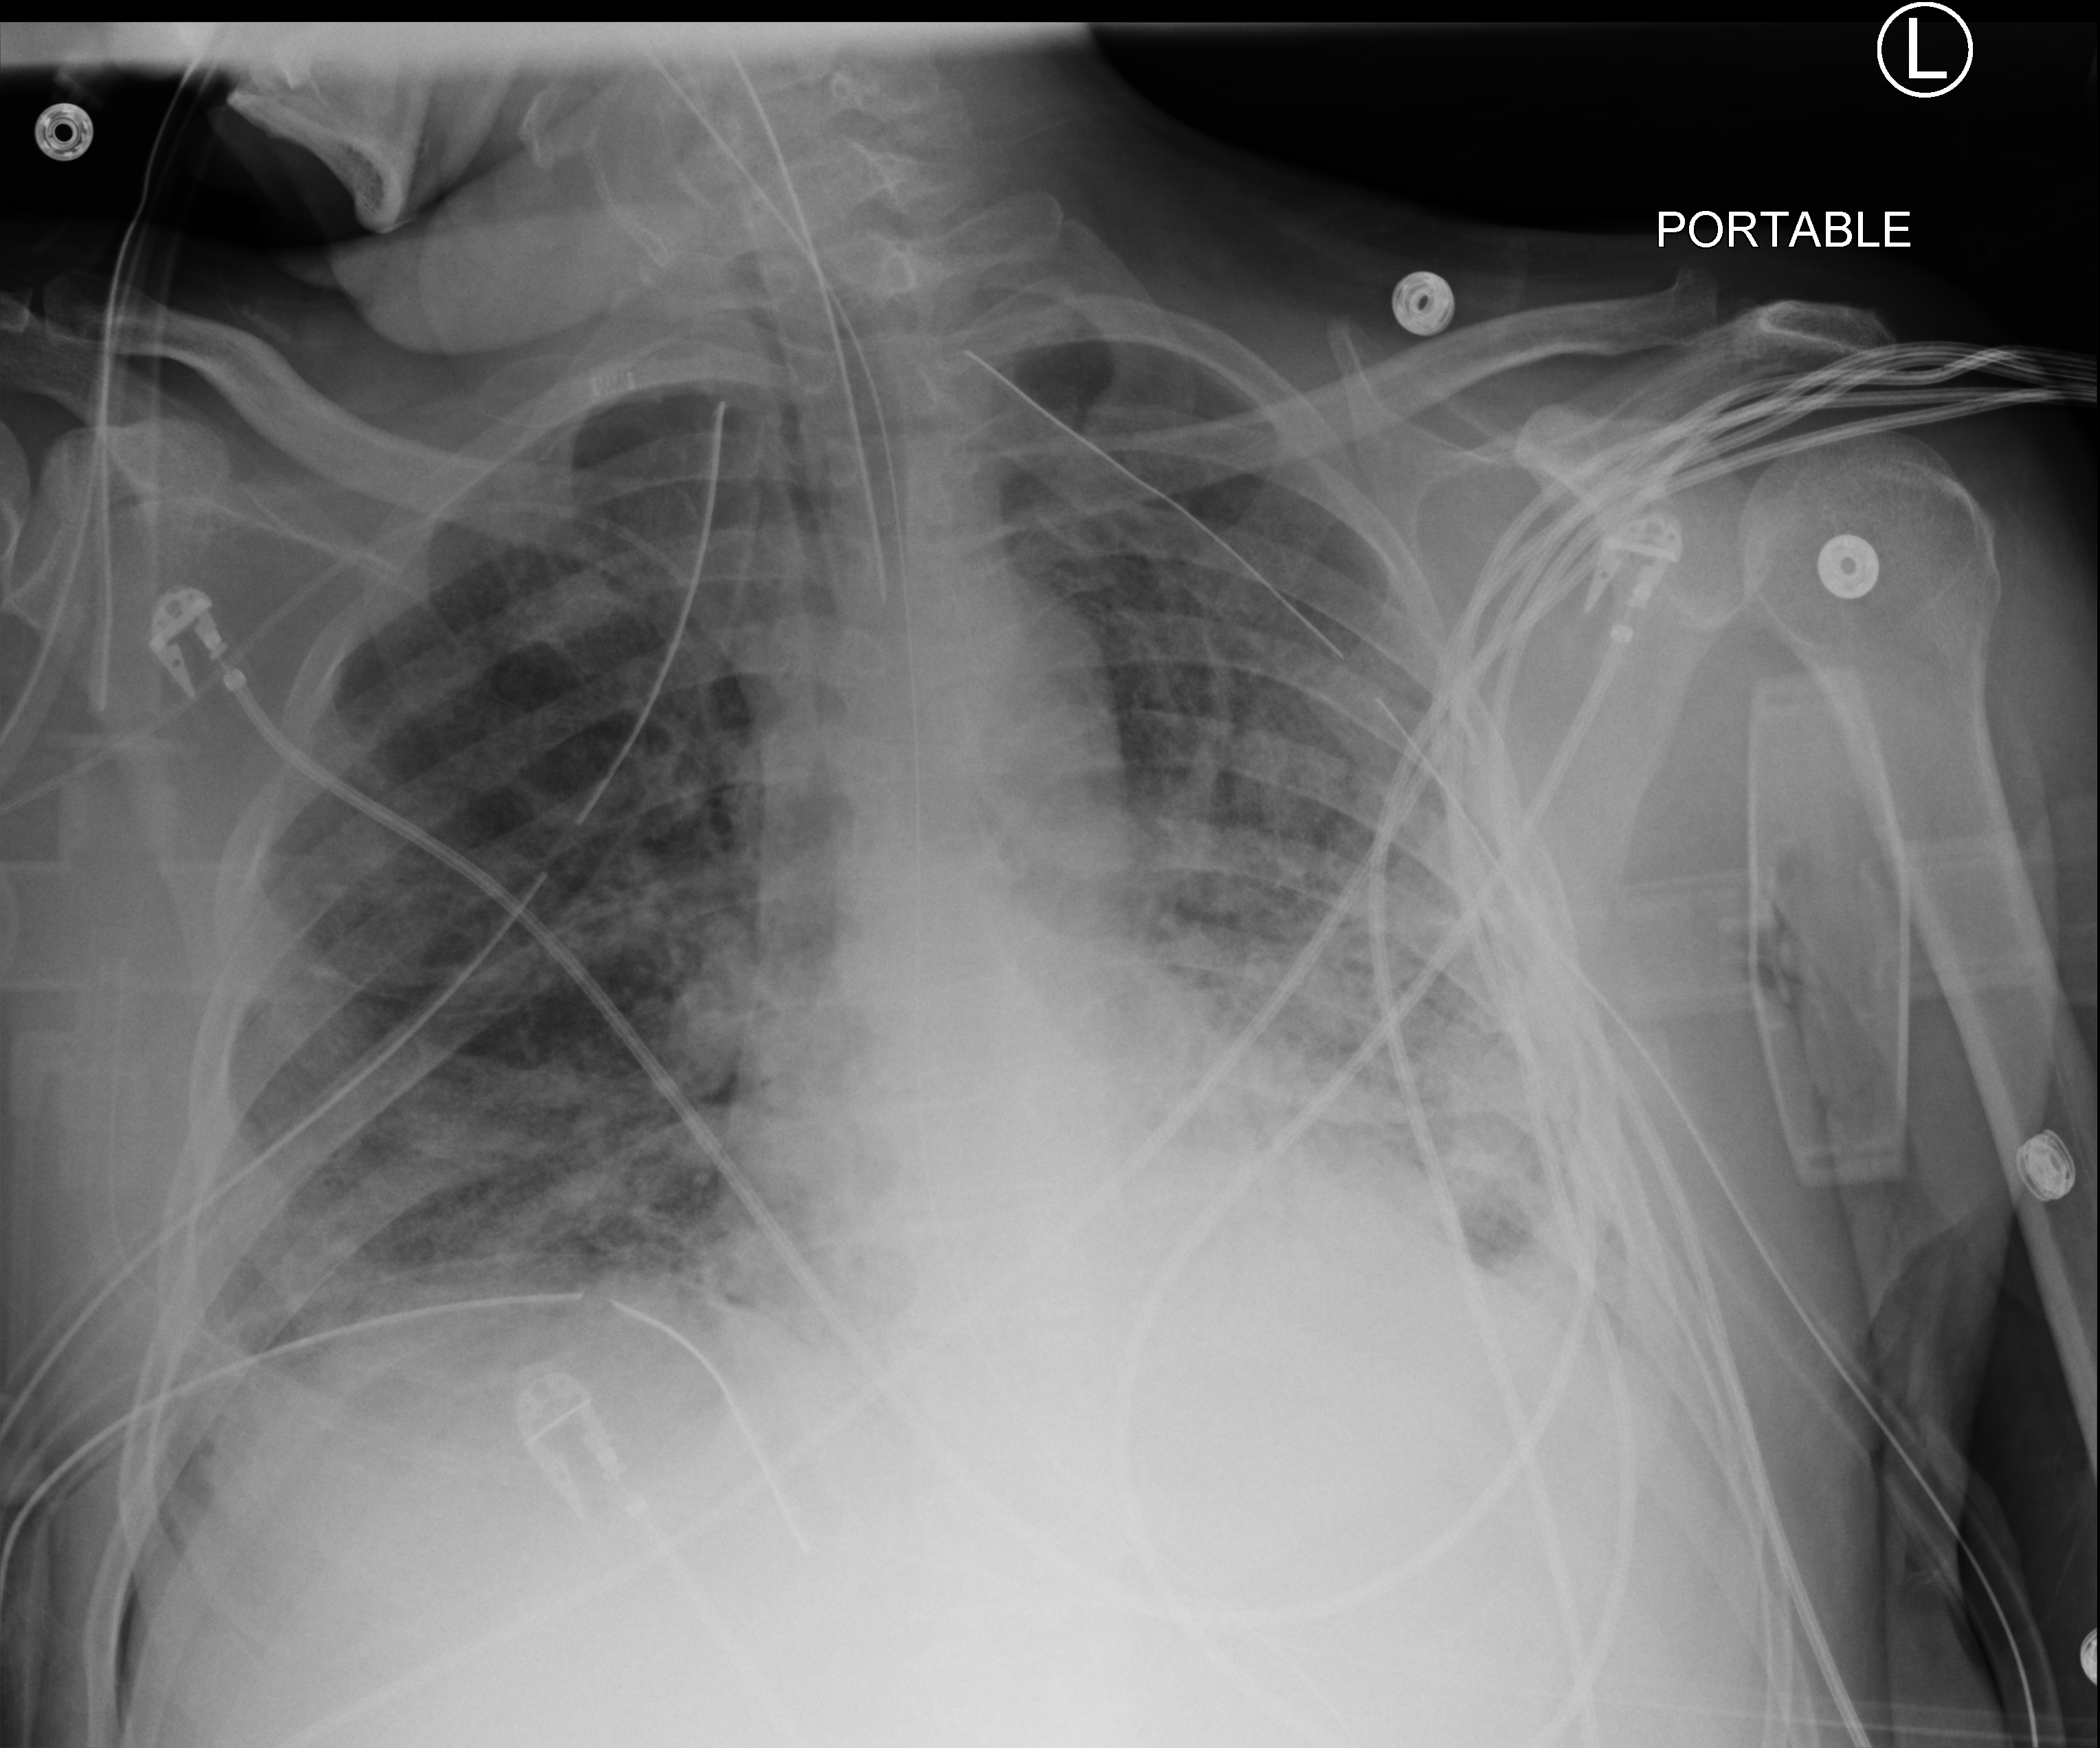
Chest X-ray (portable); anteroposterior (AP) projection. Patient hospitalised with COVID-19; male, aged 18–59 years.
Admission-level facts for this patient (not findings on this image; timing relative to this image not recorded): smoking status (admission record): never; mechanically ventilated during this hospital stay: yes.